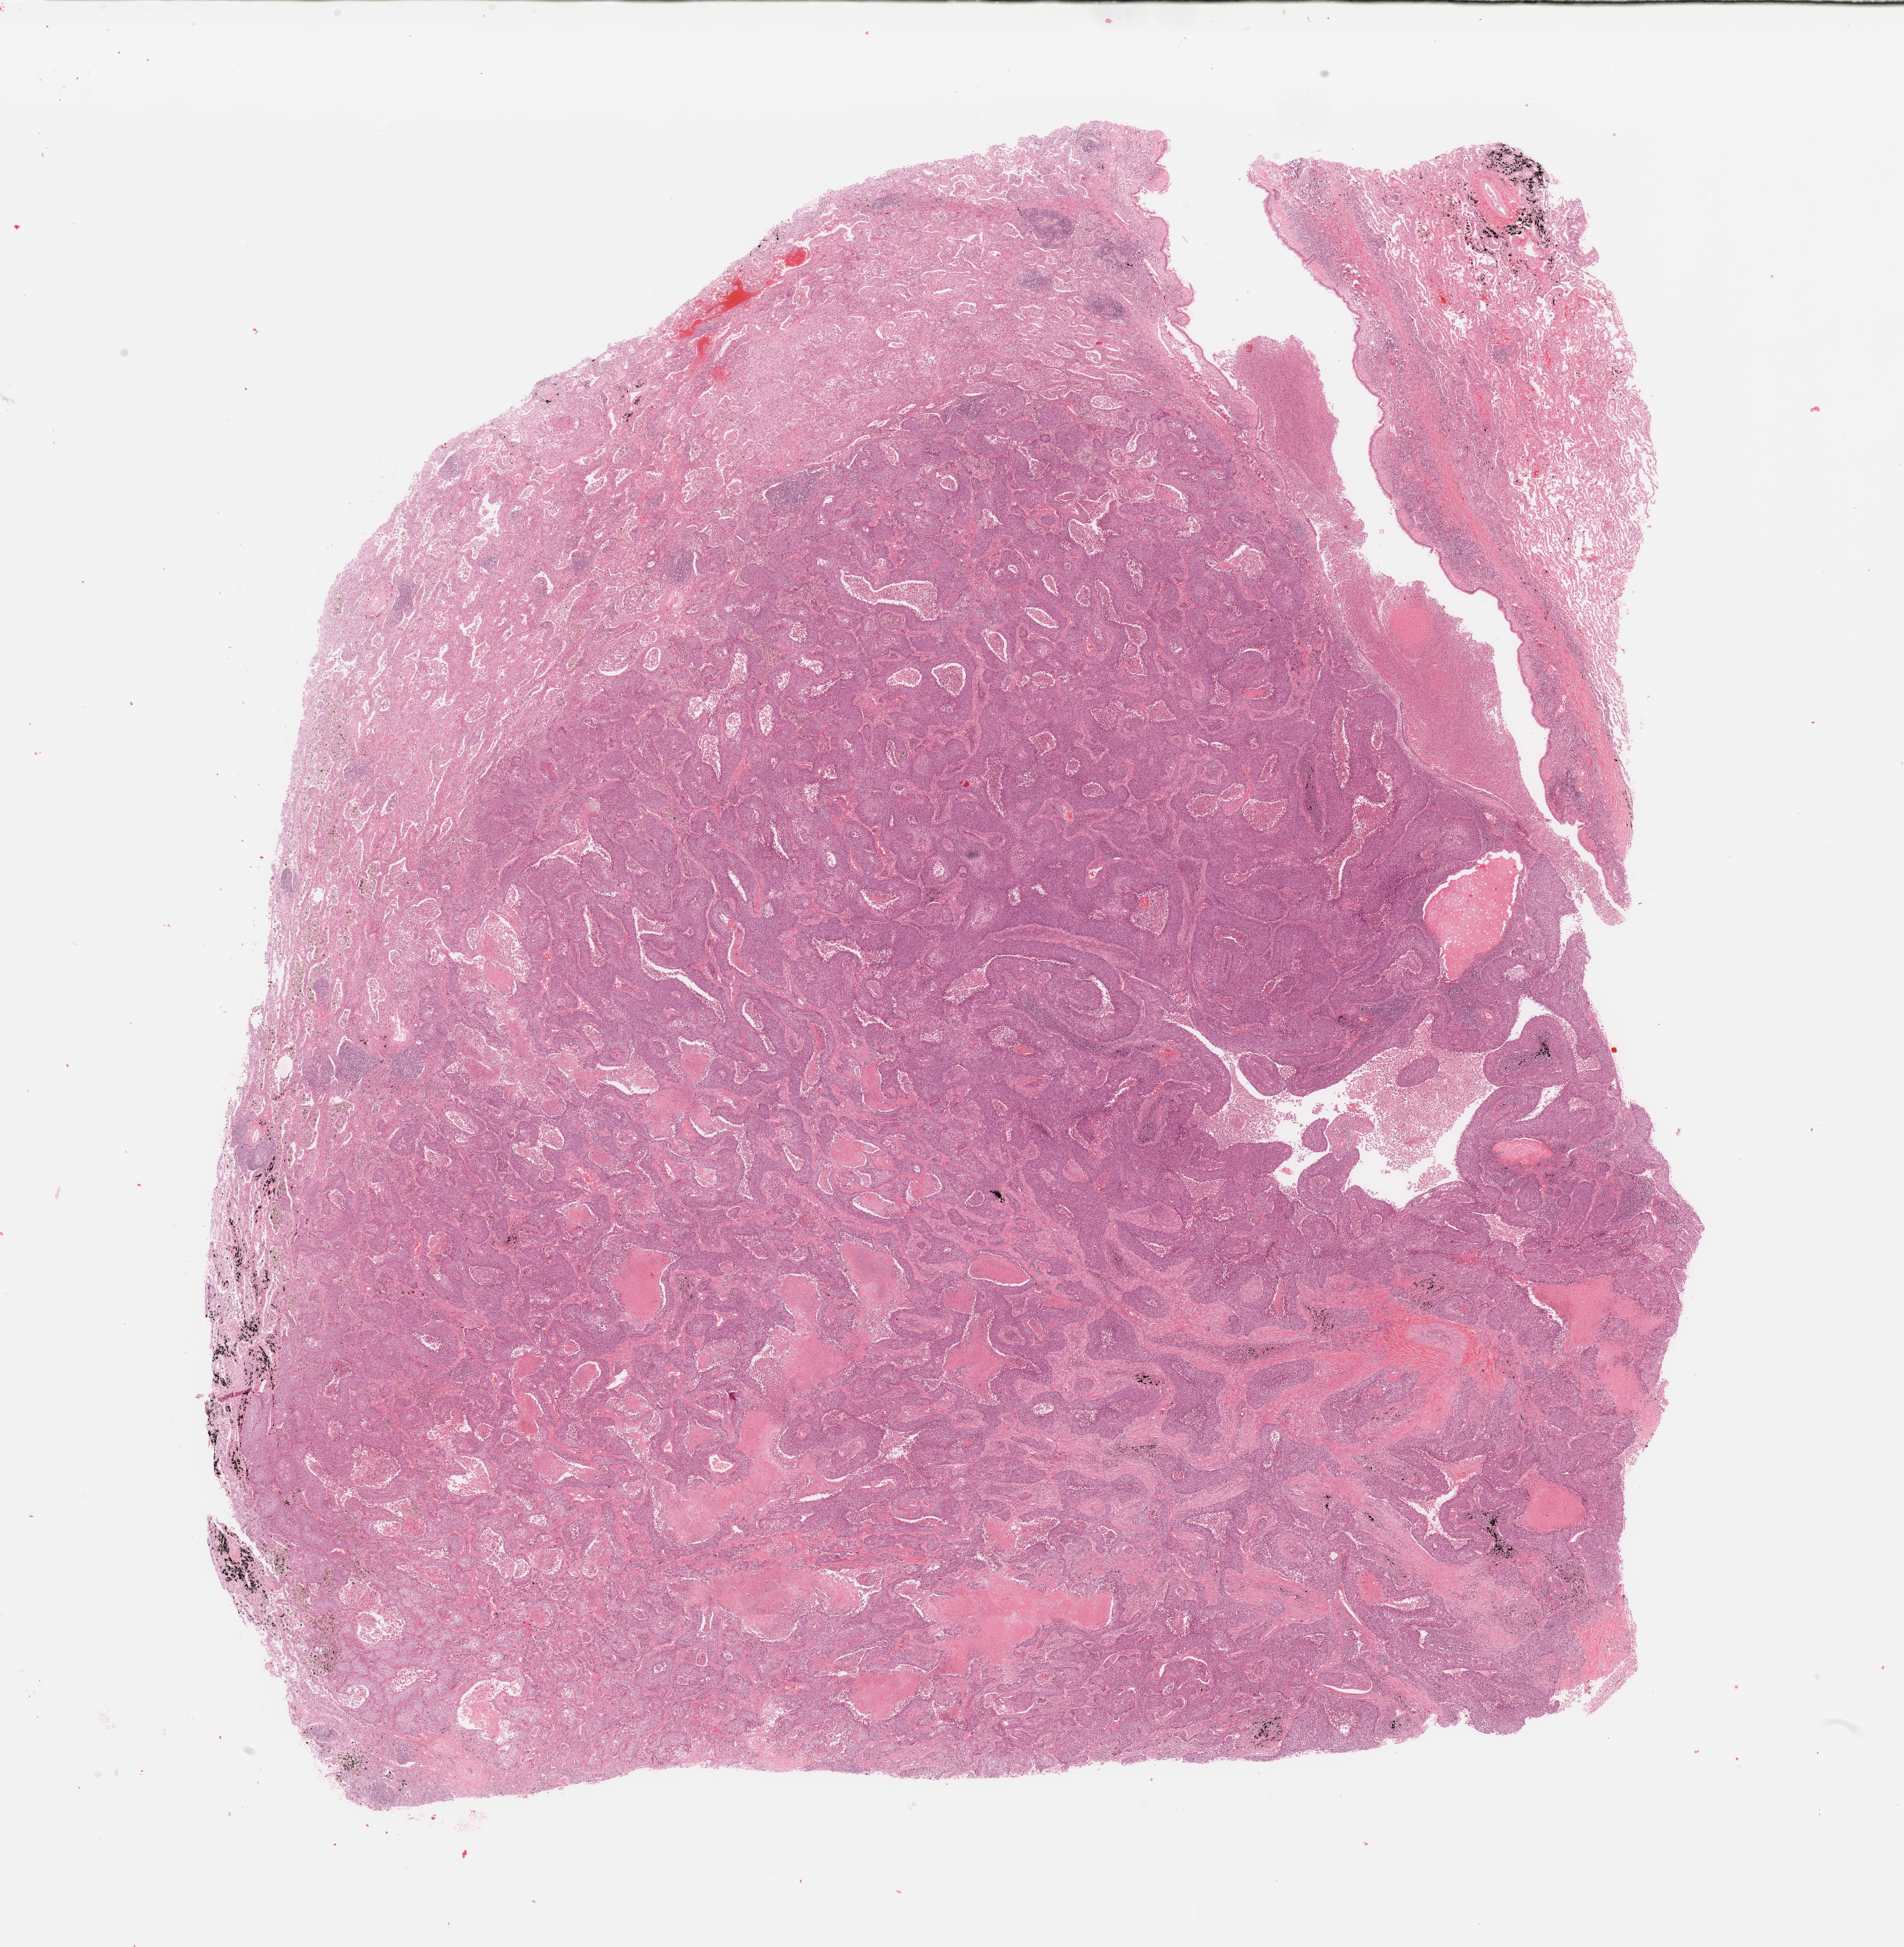
H&E whole-slide image — a low-resolution overview of the entire scanned area, about 21.7 x 22.1 mm (from a 20x scan); tumour tissue sample, sampled site: lung. 52-year-old male patient. Histologic grade: G3 (poorly differentiated). Slide review estimates, as recorded: tumour nuclei 75%, necrosis 10%.
- AJCC pathologic stage: IIB
- histologic diagnosis: Squamous cell carcinoma, NOS